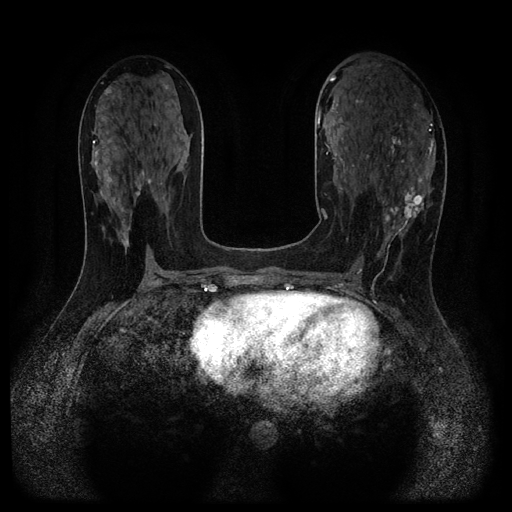
Breast MRI (dynamic contrast-enhanced, multi-phase), one axial slice. Position 54 of 116 along the scan axis. Dynamic contrast-enhanced series, time point 2 of 5 at this slice position (early post-contrast). 1.5 T. TE 2.7 ms, TR 5.4 ms. 2.2 mm slice thickness. 512 × 512 image matrix, field of view 330 × 330 mm. Female patient, age 43 years.
Outlined on this slice (semi-automatically segmented with operator editing):
- breast lesion (labelled 'tumour' in the annotation; benign lesions carry a separate 'benign' label): bounding box (x1, y1, x2, y2) in pixels: (394, 180, 429, 226)